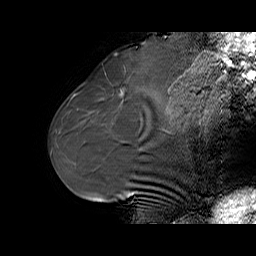
Breast MRI (dynamic contrast-enhanced), one sagittal slice. Dynamic contrast-enhanced series, time point 2 of 6 at this slice position (early post-contrast). 1.5 T. TE 5.5 ms, TR 32.9 ms. 4 mm slice thickness. 256 × 256 image matrix, field of view 240 × 240 mm. Female patient. Case-level facts recorded for this patient, not image findings: setting: breast cancer imaged before/during neoadjuvant chemotherapy; receptor status: HER2-positive.
Structures marked on this image (semi-automatically segmented with operator editing):
- analysis volume of interest (the breast-tissue region the enhancement analysis was run in; not a lesion): bounding box [x1, y1, x2, y2] px = [97, 73, 141, 114]
- tumour enhancement mask (voxels above the 100 % enhancement threshold inside the analysis volume of interest): [121, 91, 123, 94]